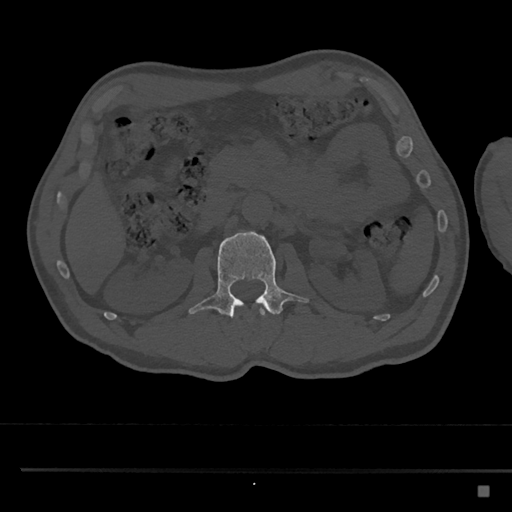
CT including the spine, one axial slice; slice 771 of 797 in the series (ordered by position); reconstruction kernel Br40s/3; bone window (W 1800 / L 400 HU); 0.5 mm slice thickness; 512 × 512 image matrix, field of view 391 × 391 mm. Patient: male, 59 years. From the clinical record (not read from this slice): primary cancer: prostate.
Annotated regions visible in this slice (semi-automatic segmentation, software-assisted and operator-edited):
- L1 vertebra: box from (x=261, y=311) to (x=265, y=315) px
- L2 vertebra: (x=188, y=231)–(x=309, y=318)